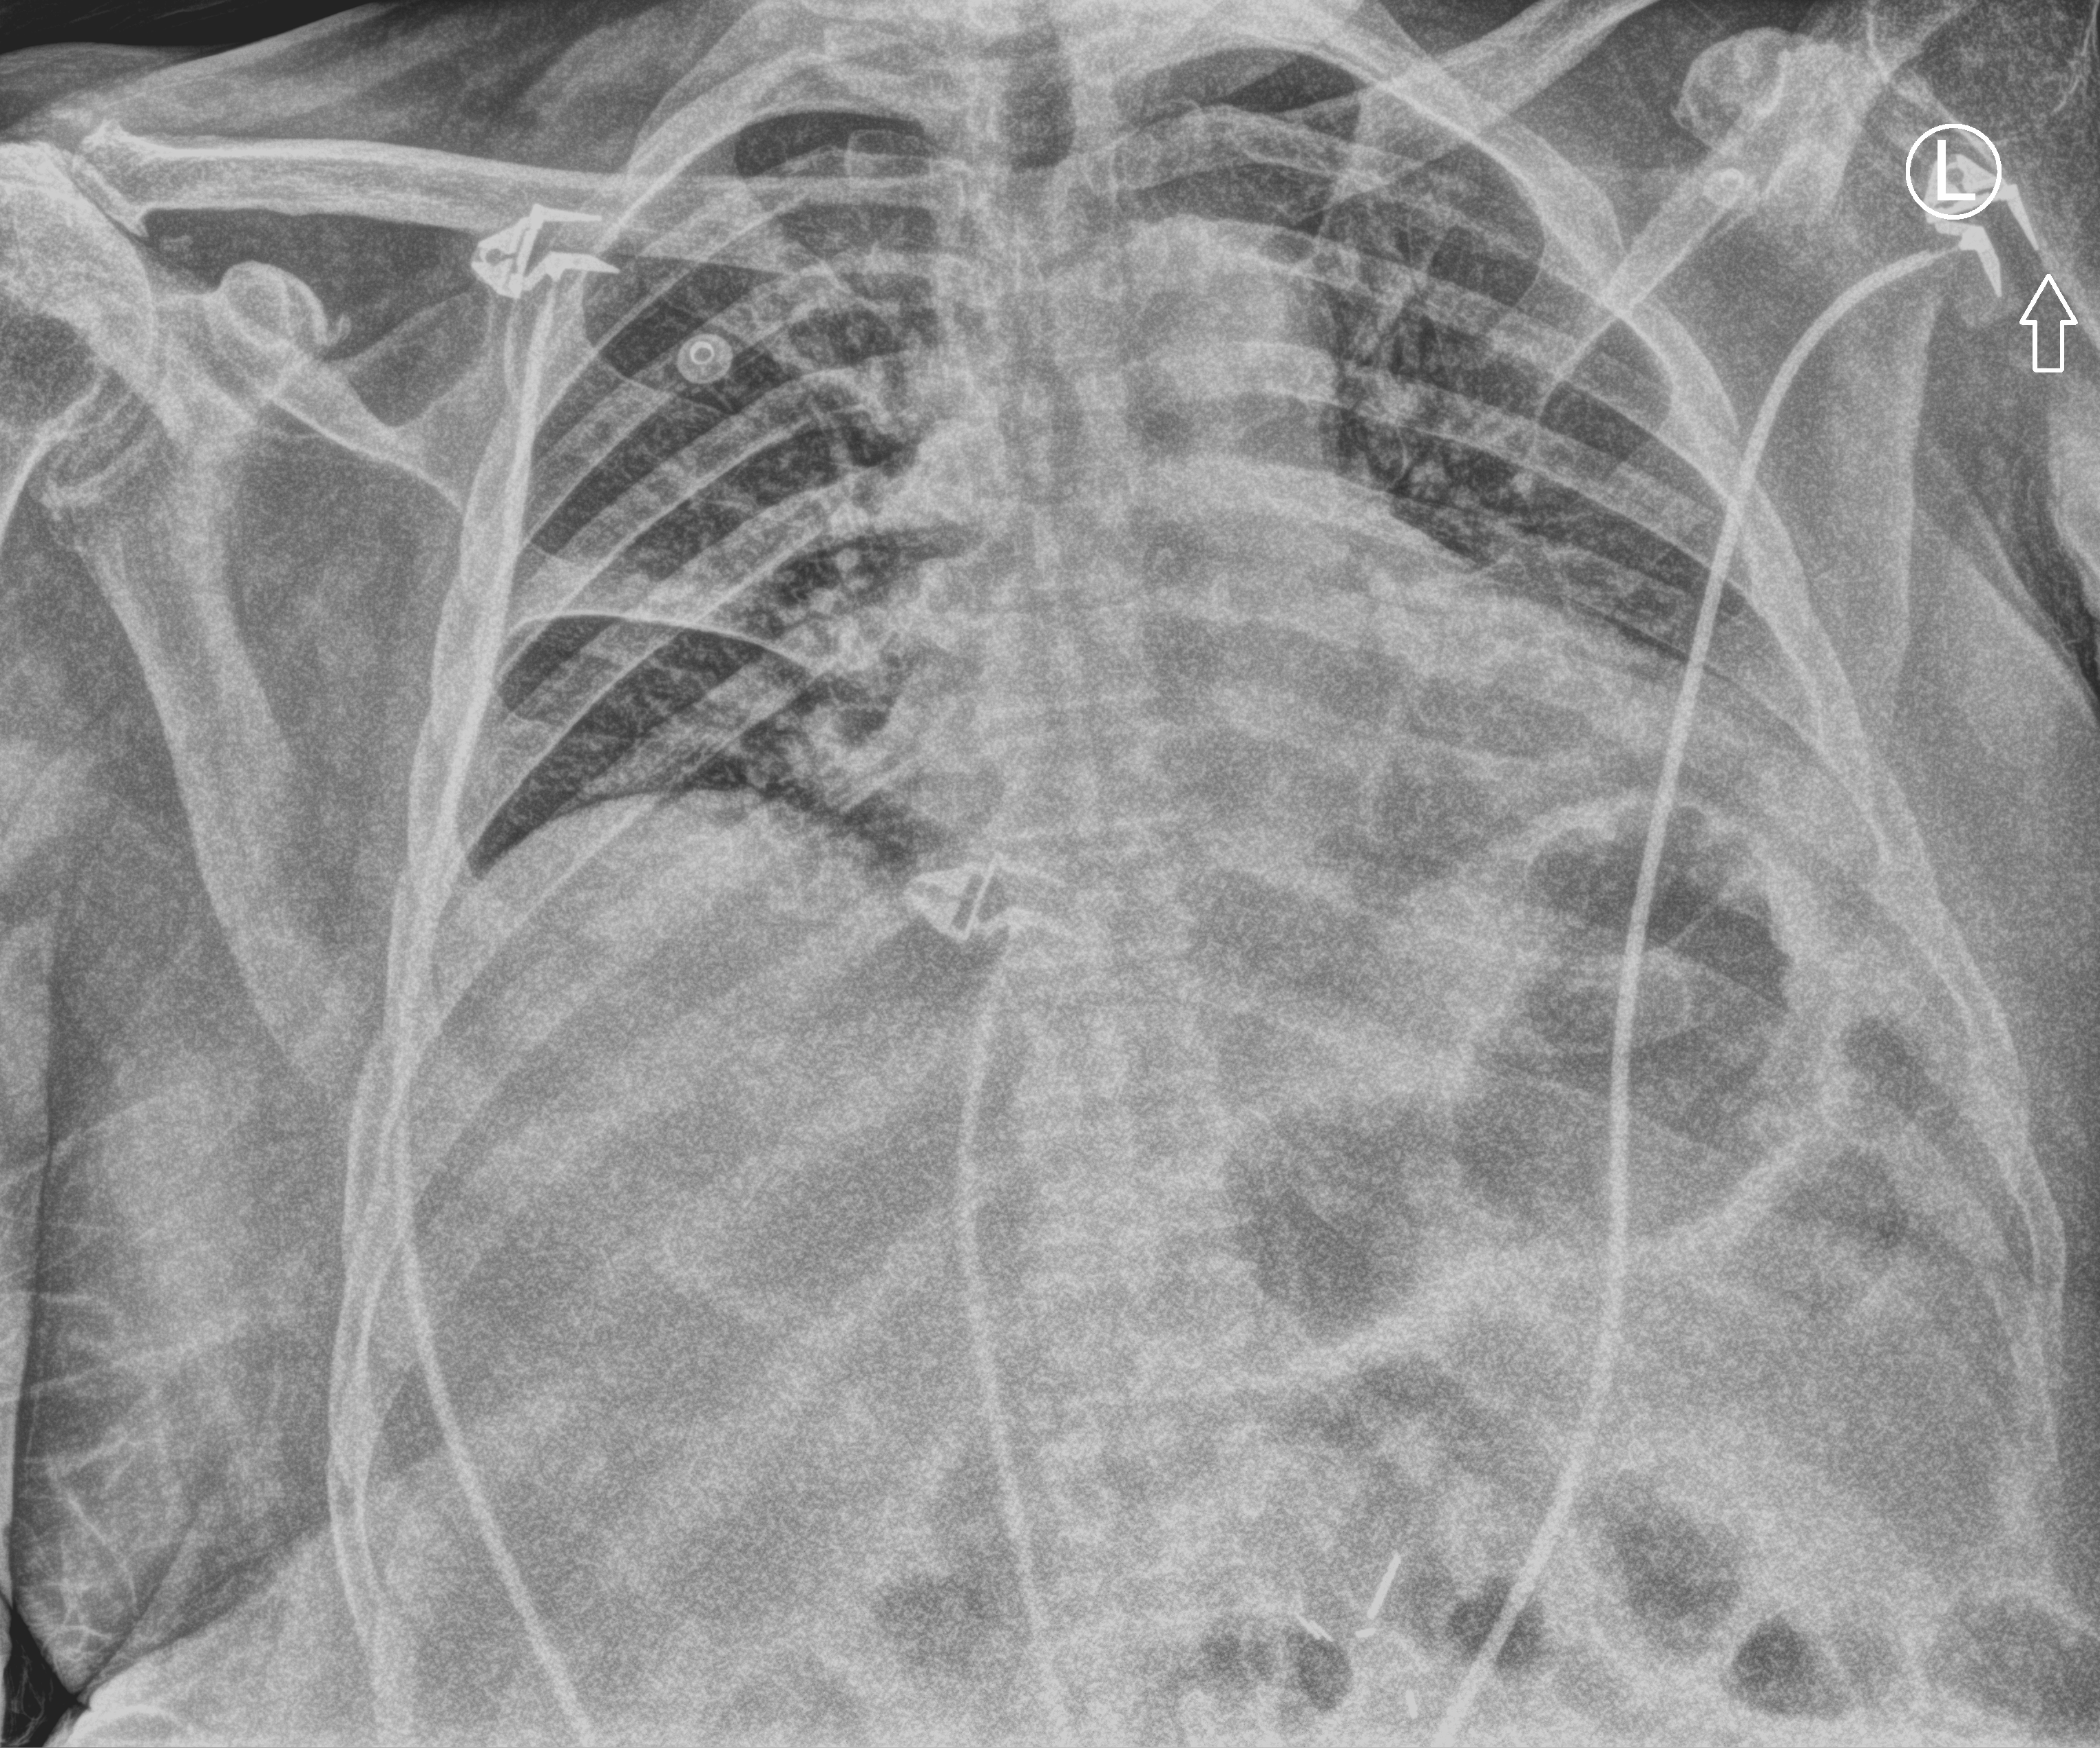
Portable chest radiograph, anteroposterior (AP) projection. Patient hospitalised with COVID-19; male, aged 75–90 years.
Admission-level facts for this patient (not findings on this image; timing relative to this image not recorded):
- chronic kidney disease (admission record): no
- length of hospital stay: 12 days